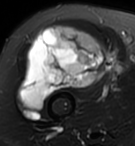
MRI of an extremity soft-tissue mass, one axial slice; position 66 of 95 along the scan axis; T2-weighted fat-saturated; MR volume resampled by the dataset authors to the PET/CT grid (not the native acquisition matrix); 3.27 mm slice thickness; 135 × 146 image matrix, field of view 132 × 143 mm. Female patient. Case-level facts recorded for this patient, not image findings: histological type: pleiomorphic undifferentiated sarcoma; grade: high; site of the primary tumour: right quadricep.
Outlined on this slice (expert contour drawn on MRI and transferred to this co-registered scan by the dataset authors):
- gross tumour volume including surrounding oedema: box from (x=19, y=25) to (x=109, y=110) px
- gross tumour volume (mass): (x=19, y=25)–(x=109, y=110)